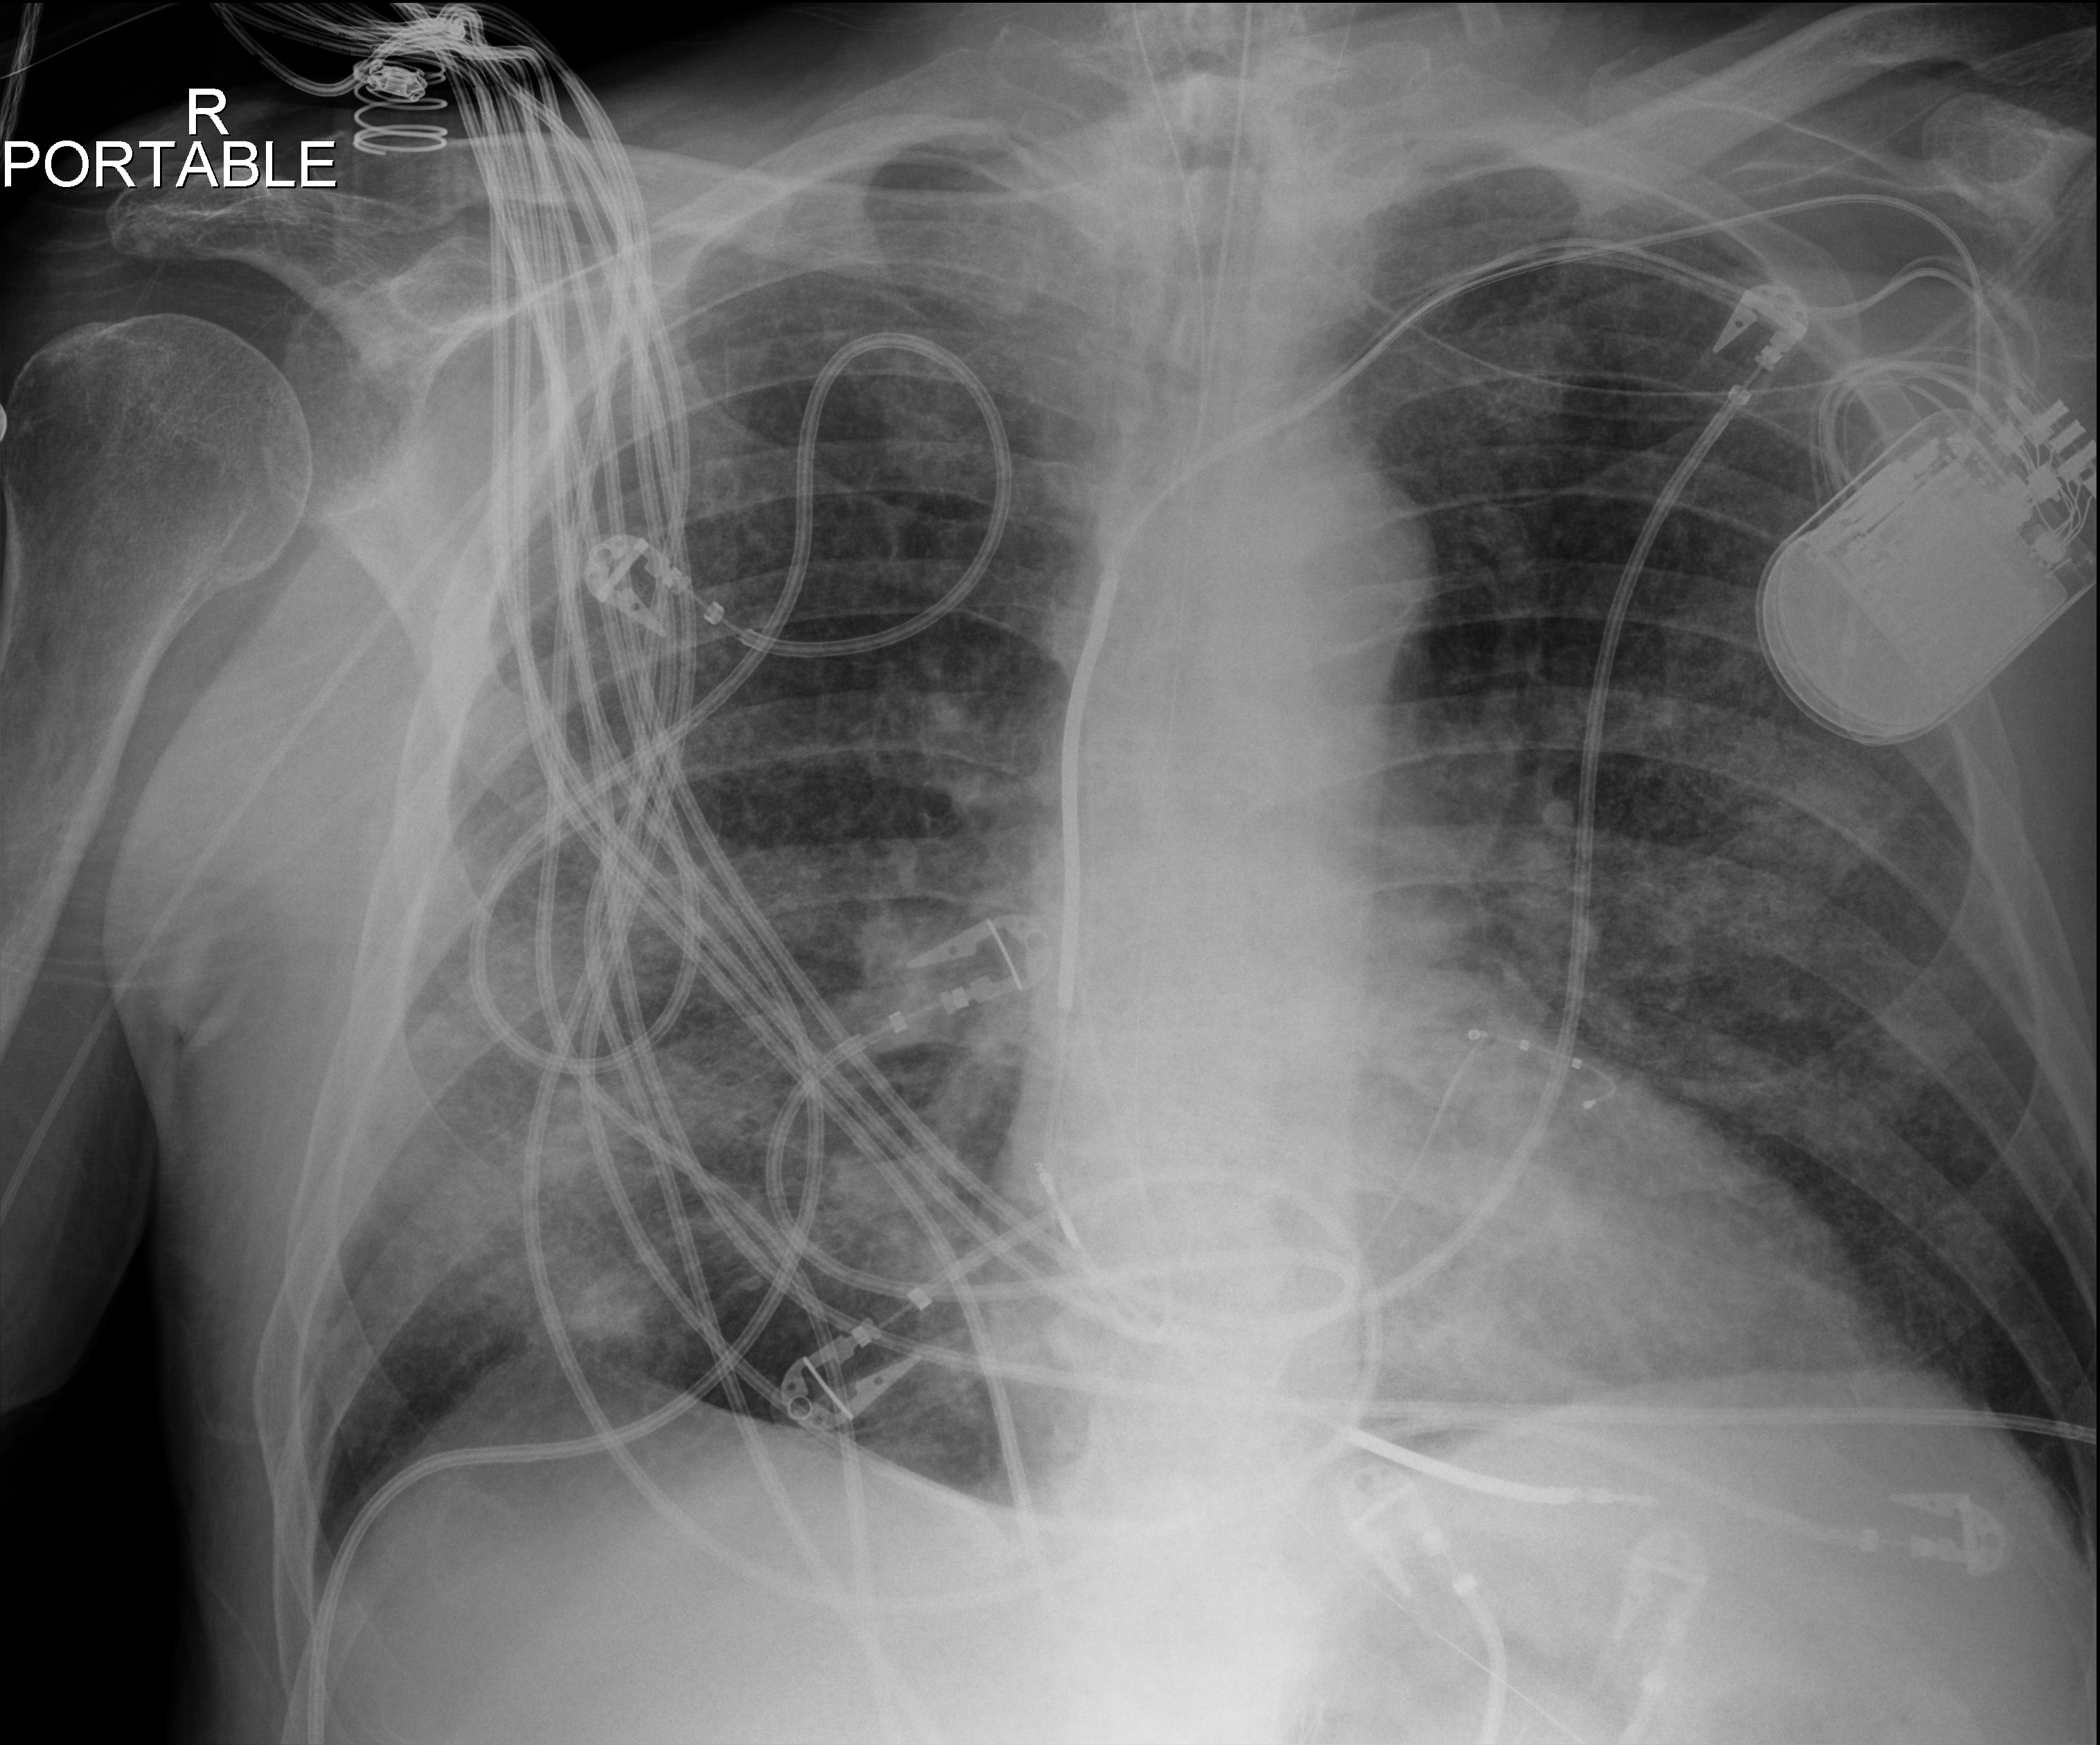
Bedside chest radiograph (digital radiography); anteroposterior (AP) projection. Patient hospitalised with COVID-19; male, aged 60–74 years.
From the hospital-stay record, not from the radiograph (when in the stay this image was taken is not recorded): admitted to intensive care during this hospital stay: yes.